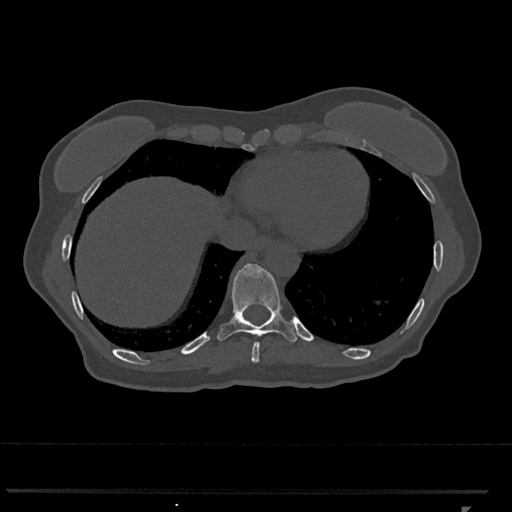
CT including the spine, one axial slice. Reconstruction kernel Br40s/3. 120 kVp. Bone window (W 1800 / L 400 HU). 0.5 mm slice thickness. 512 × 512 image matrix. Patient: female, 62 years. Case-level facts recorded for this patient, not image findings: primary cancer: renal.
Annotated regions visible in this slice (semi-automatically segmented with operator editing):
- T10 vertebra: bounding box [x1, y1, x2, y2] px = [217, 263, 298, 342]
- T9 vertebra: [251, 343, 259, 363]